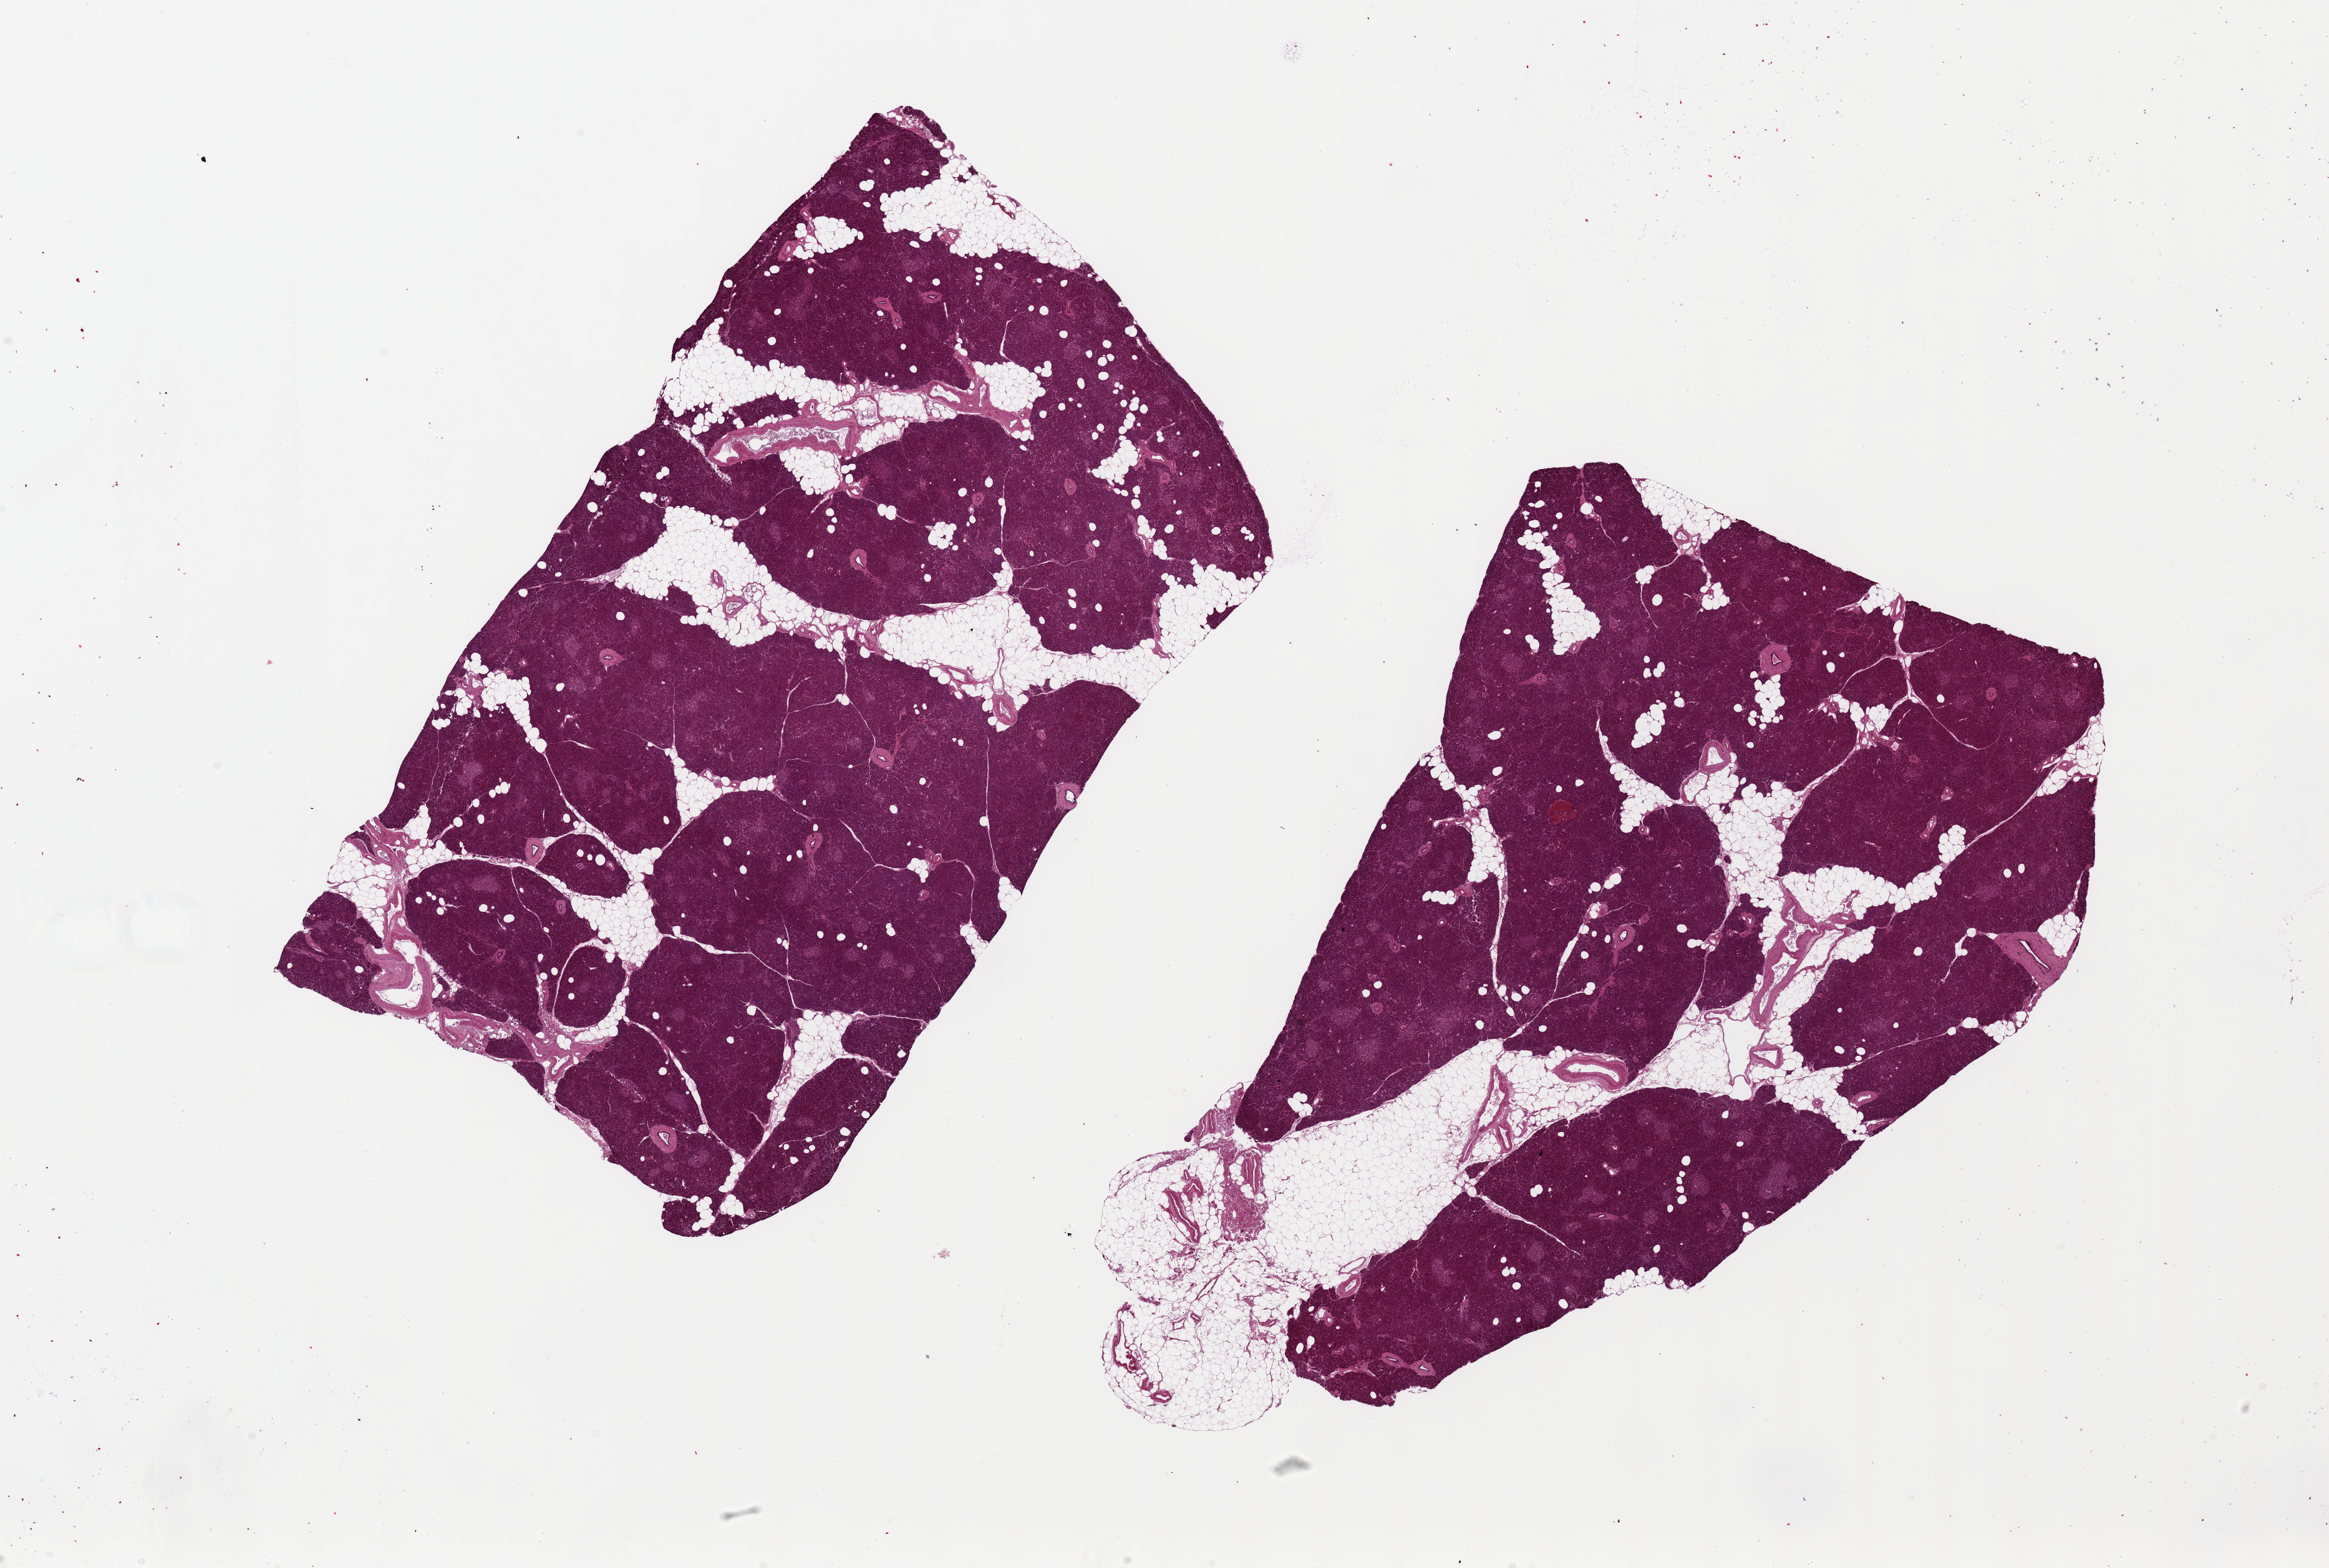
Haematoxylin and eosin whole-slide image, whole scanned area (about 29.5 x 19.9 mm) shown as a low-resolution overview; PAXgene-fixed paraffin-embedded (PFPE) section; section of pancreas (target tissue); donor tissue sample. Donor sex: male.
Pathologist's review note for this sample: 2 pieces ~12x8mm, extremely well preserved, Islets well seen, several.